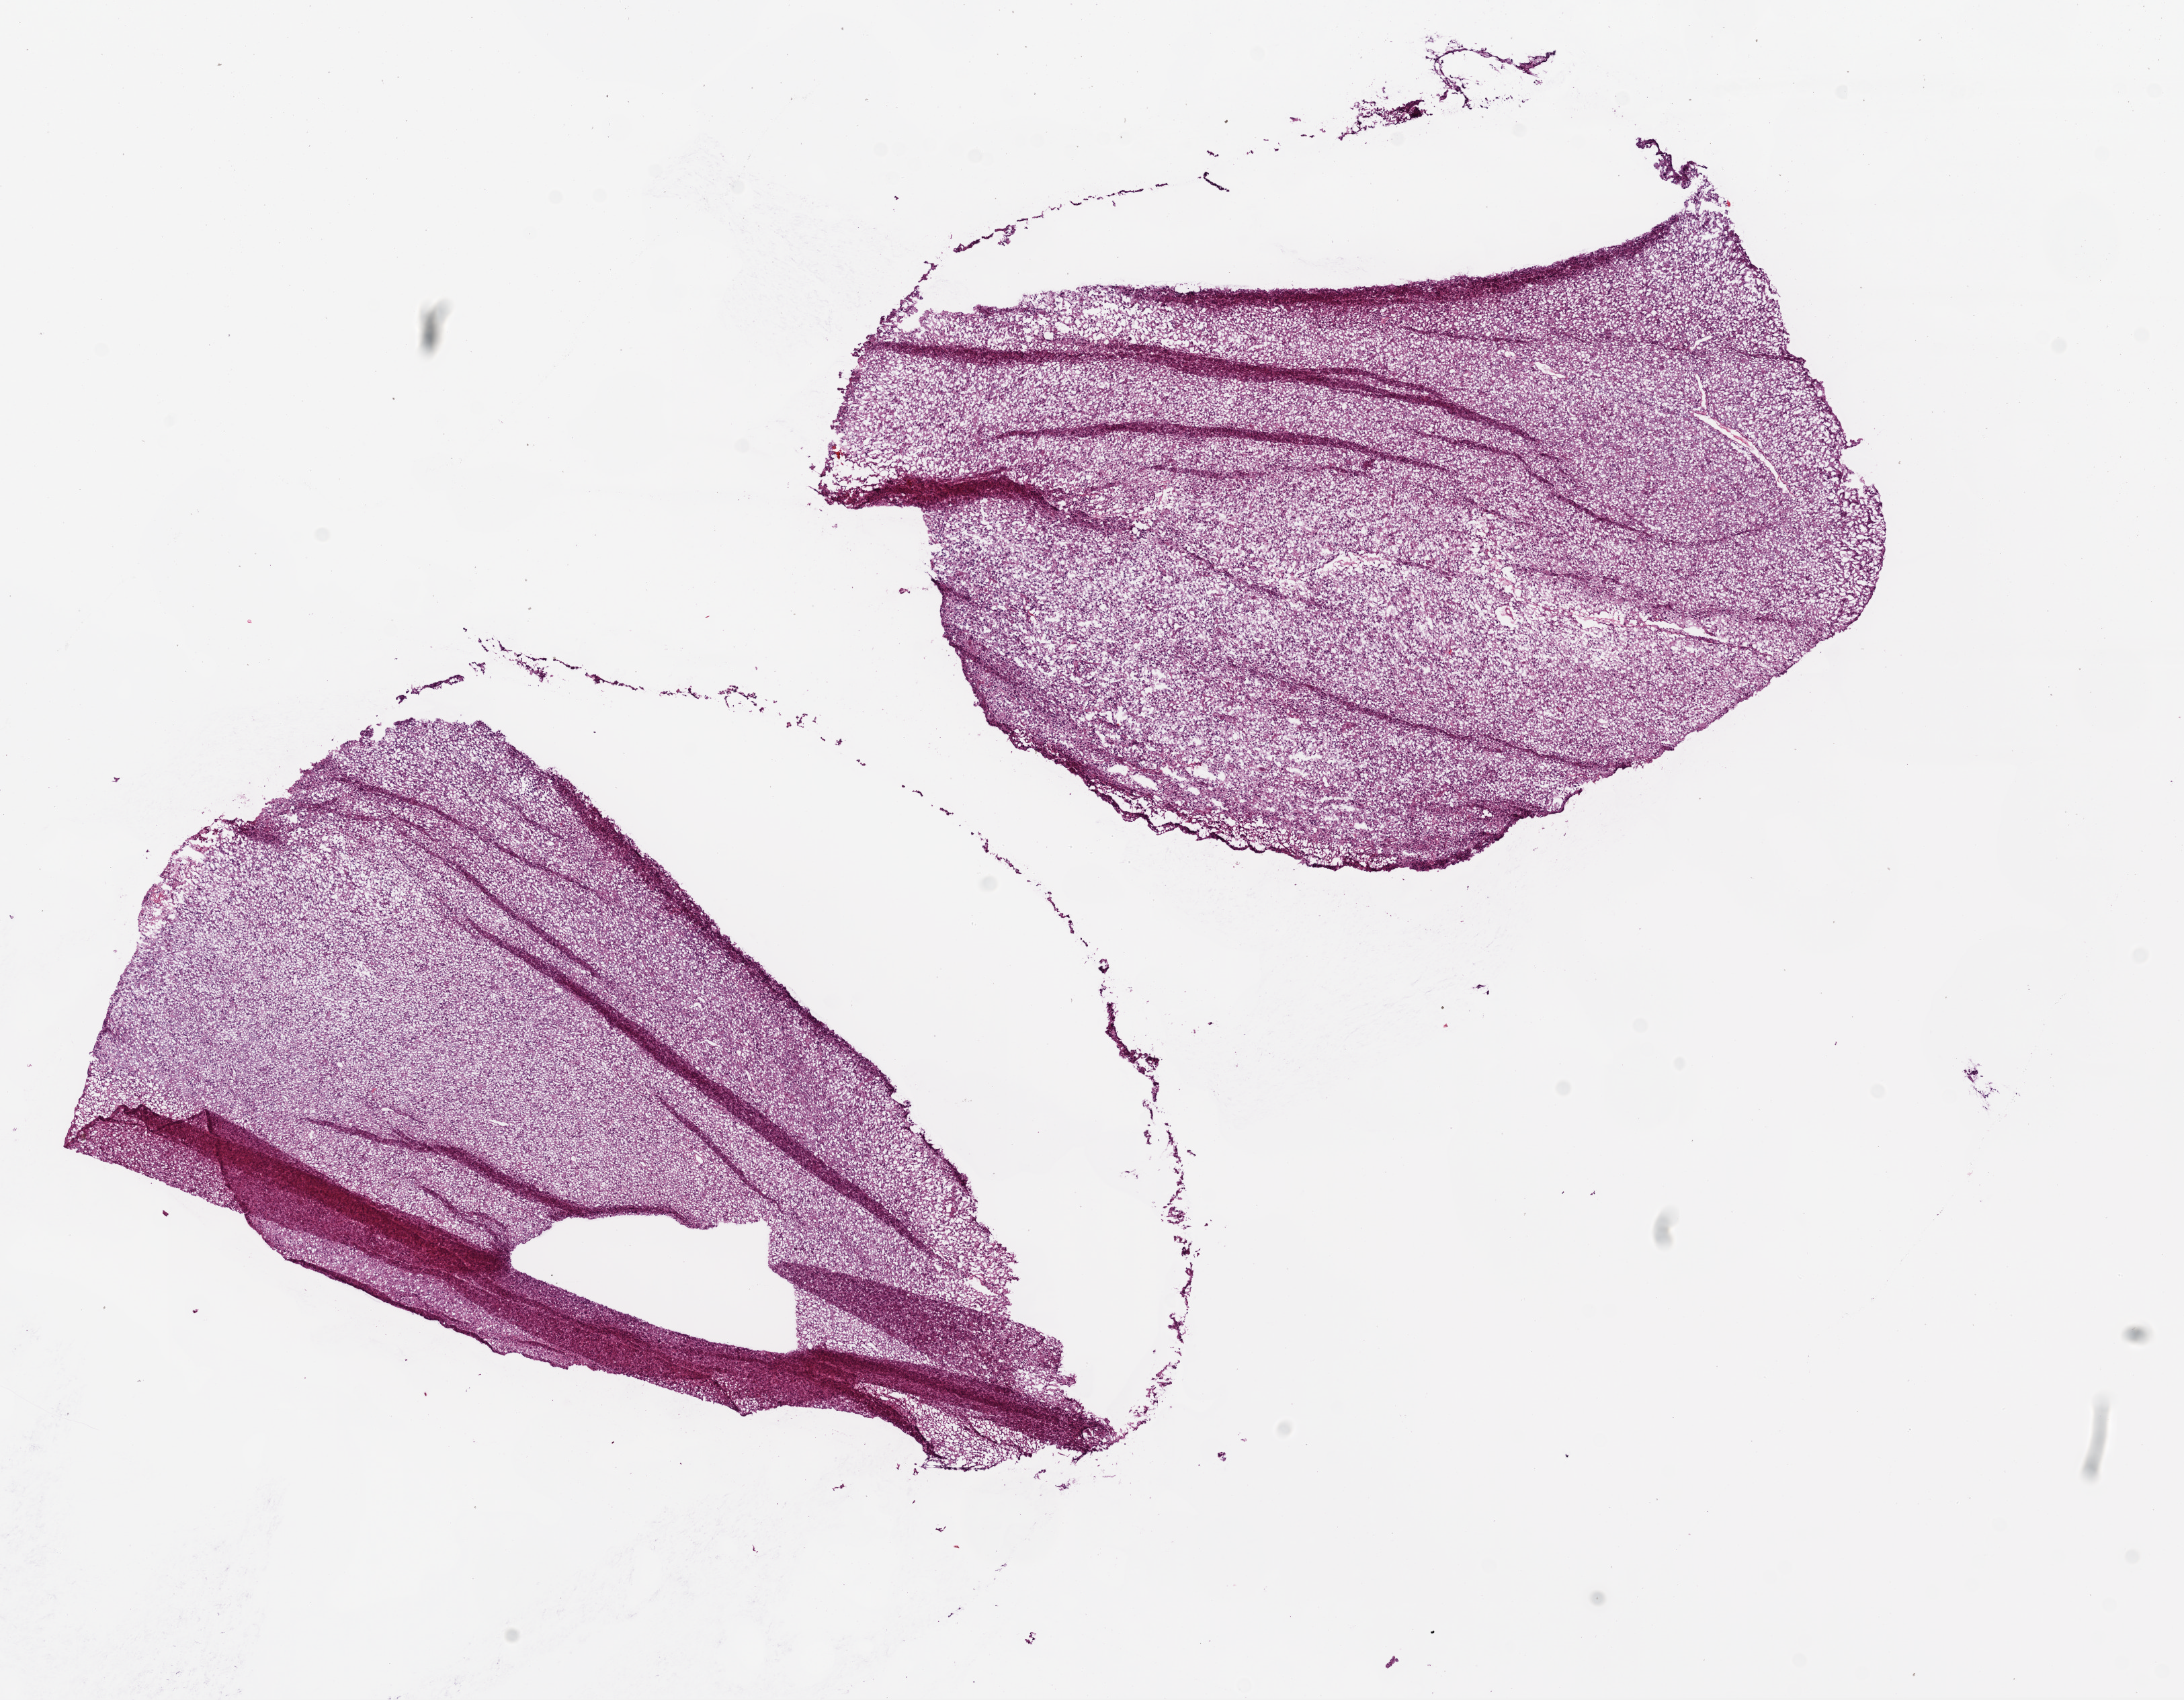
H&E whole-slide image — shown as a low-resolution overview of the whole scanned area (about 13.0 x 10.2 mm), frozen section from the bottom of the tissue portion, brain, primary tumour sample. Patient: female, age at initial diagnosis 64 years. Slide review estimates, as recorded: tumour cells 100%, tumour nuclei 80%, normal cells 0%, stromal cells 0%, necrosis 0%.
* pathologic diagnosis: Glioblastoma